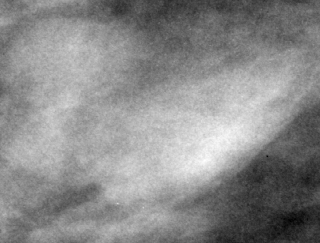
Cropped region of a digitized screen-film mammogram centred on a radiologist-marked abnormality; right breast; MLO view; BI-RADS breast density category 3 (scale 1–4).
Mass, shape irregular, margins circumscribed / ill defined; BI-RADS assessment category 4; subtlety rating 4 on a 1 (subtle) to 5 (obvious) scale; pathology (as recorded): benign.